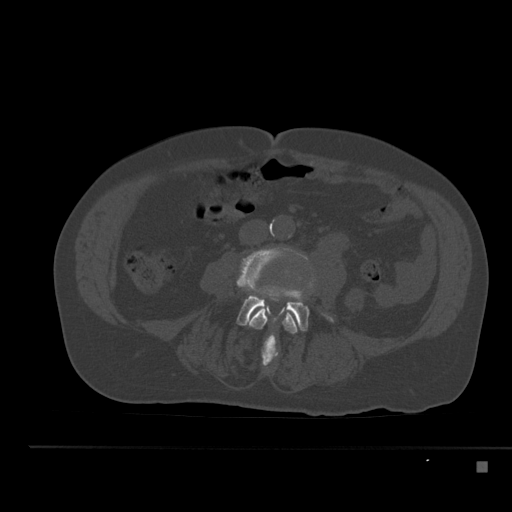
CT including the spine, one axial slice; position 151 of 517 along the scan axis; reconstruction kernel Br40s; bone window (W 1800 / L 400 HU); 1.5 mm slice thickness; 512 × 512 image matrix. Patient: male, 70 years. Case-level facts recorded for this patient, not image findings: primary cancer: renal.
Structures marked on this image (semi-automatic segmentation, software-assisted and operator-edited):
- L3 vertebra: bounding box <238,247,298,366> (left, top, right, bottom; pixels)
- L4 vertebra: <237,284,332,331>